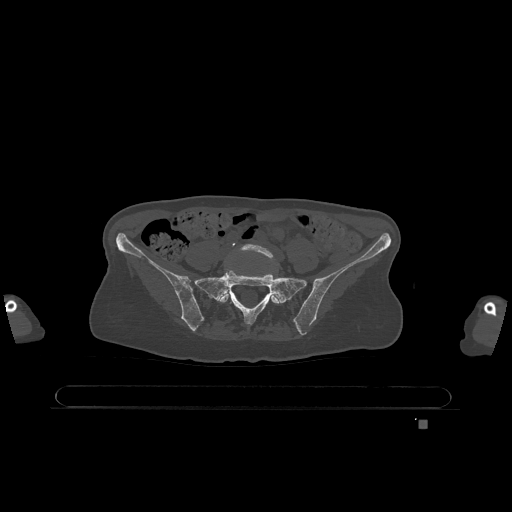
CT including the spine, one axial slice; position 206 of 1317 along the scan axis; bone window (W 1800 / L 400 HU); 0.5 mm slice thickness; 512 × 512 image matrix, field of view 500 × 500 mm. Female patient, age 74 years. From the clinical record (not read from this slice): primary cancer: lung; vertebrae with lytic lesions (as recorded): T1, T4, T5, T6, L4, L5.
Annotated regions visible in this slice (semi-automatic segmentation, software-assisted and operator-edited):
- L5 vertebra: bounding box <219,244,280,304> (left, top, right, bottom; pixels)